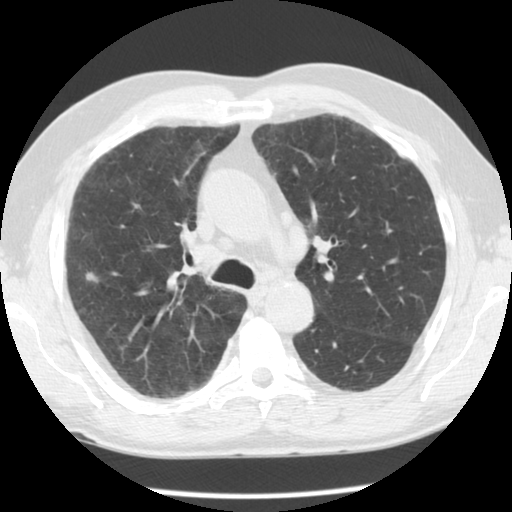
Low-dose screening chest CT, one axial slice. Slice 75 of 113 in the series (ordered by position). Reconstruction kernel STANDARD. Lung window (W 1500 / L -600 HU). 2.5 mm slice thickness. 512 × 512 image matrix.
Outlined on this slice (outlined manually by an expert reader):
- lesion 2 (nodule): bounding box (x1, y1, x2, y2) in pixels: (86, 272, 98, 283)